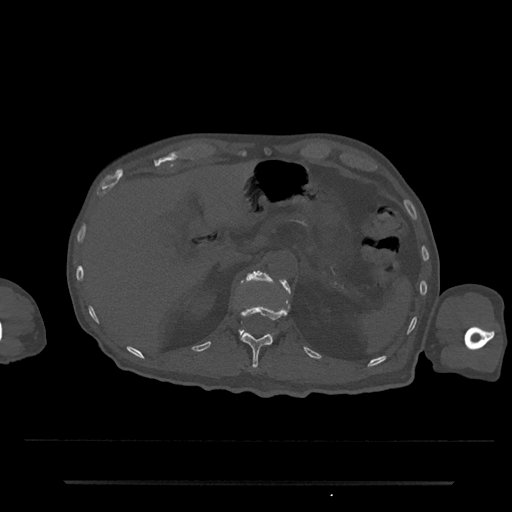
CT including the spine, one axial slice; position 177 of 797 along the scan axis; 120 kVp; bone window (W 1800 / L 400 HU); 0.5 mm slice thickness; 512 × 512 image matrix, field of view 427 × 427 mm. Male patient, age 74 years. From the clinical record (not read from this slice): primary cancer: prostate.
Outlined on this slice (semi-automatically segmented with operator editing):
- L1 vertebra: bounding box [x1, y1, x2, y2] px = [239, 271, 291, 337]
- T12 vertebra: [240, 306, 288, 370]